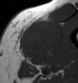
MRI of an extremity soft-tissue mass, one axial slice. Position 25 of 43 along the scan axis. MR volume resampled by the dataset authors to the PET/CT grid (not the native acquisition matrix). 78 × 83 image matrix, field of view 76 × 81 mm. Male patient. From the clinical record (not read from this slice): histological type: pleiomorphic leiomyosarcoma; grade: high; site of the primary tumour: left thigh.
Annotated regions visible in this slice (expert contour drawn on MRI and transferred to this co-registered scan by the dataset authors):
- gross tumour volume including surrounding oedema: bounding box <18,19,57,63> (left, top, right, bottom; pixels)
- gross tumour volume (mass): <20,24,51,61>